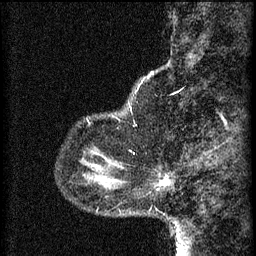
Breast MRI (dynamic contrast-enhanced), one sagittal slice. Slice 10 of 60 in the series (ordered by position). 3 images stored at this slice position (order not interpretable as contrast timing). 1.5 T. TE 4.2 ms, TR 8.2 ms. 2 mm slice thickness. 256 × 256 image matrix. Female patient, age 37 years.
Annotated regions visible in this slice (semi-automatic segmentation, software-assisted and operator-edited):
- analysis volume of interest (the breast-tissue region the enhancement analysis was run in; not a lesion): bounding box <157,176,171,191> (left, top, right, bottom; pixels)
- tumour enhancement mask (voxels above the 70 % enhancement threshold inside the analysis volume of interest): <161,180,168,185>